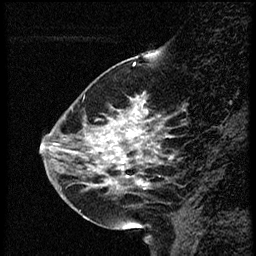
Breast MRI (dynamic contrast-enhanced), one sagittal slice. Dynamic contrast-enhanced study with each time point stored as its own series, time point 2 of 4 at this slice position (early post-contrast, ordered by acquisition time). 1.5 T. TE 4.2 ms, TR 18.9 ms. 2 mm slice thickness. 256 × 256 image matrix. Female patient. From the clinical record (not read from this slice): setting: breast cancer imaged before/during neoadjuvant chemotherapy; receptor status: HER2-positive.
Annotated regions visible in this slice (semi-automatically segmented with operator editing):
- analysis volume of interest (the breast-tissue region the enhancement analysis was run in; not a lesion): box from (x=63, y=80) to (x=169, y=215) px
- tumour enhancement mask (voxels above the 100 % enhancement threshold inside the analysis volume of interest): (x=91, y=96)–(x=150, y=189)